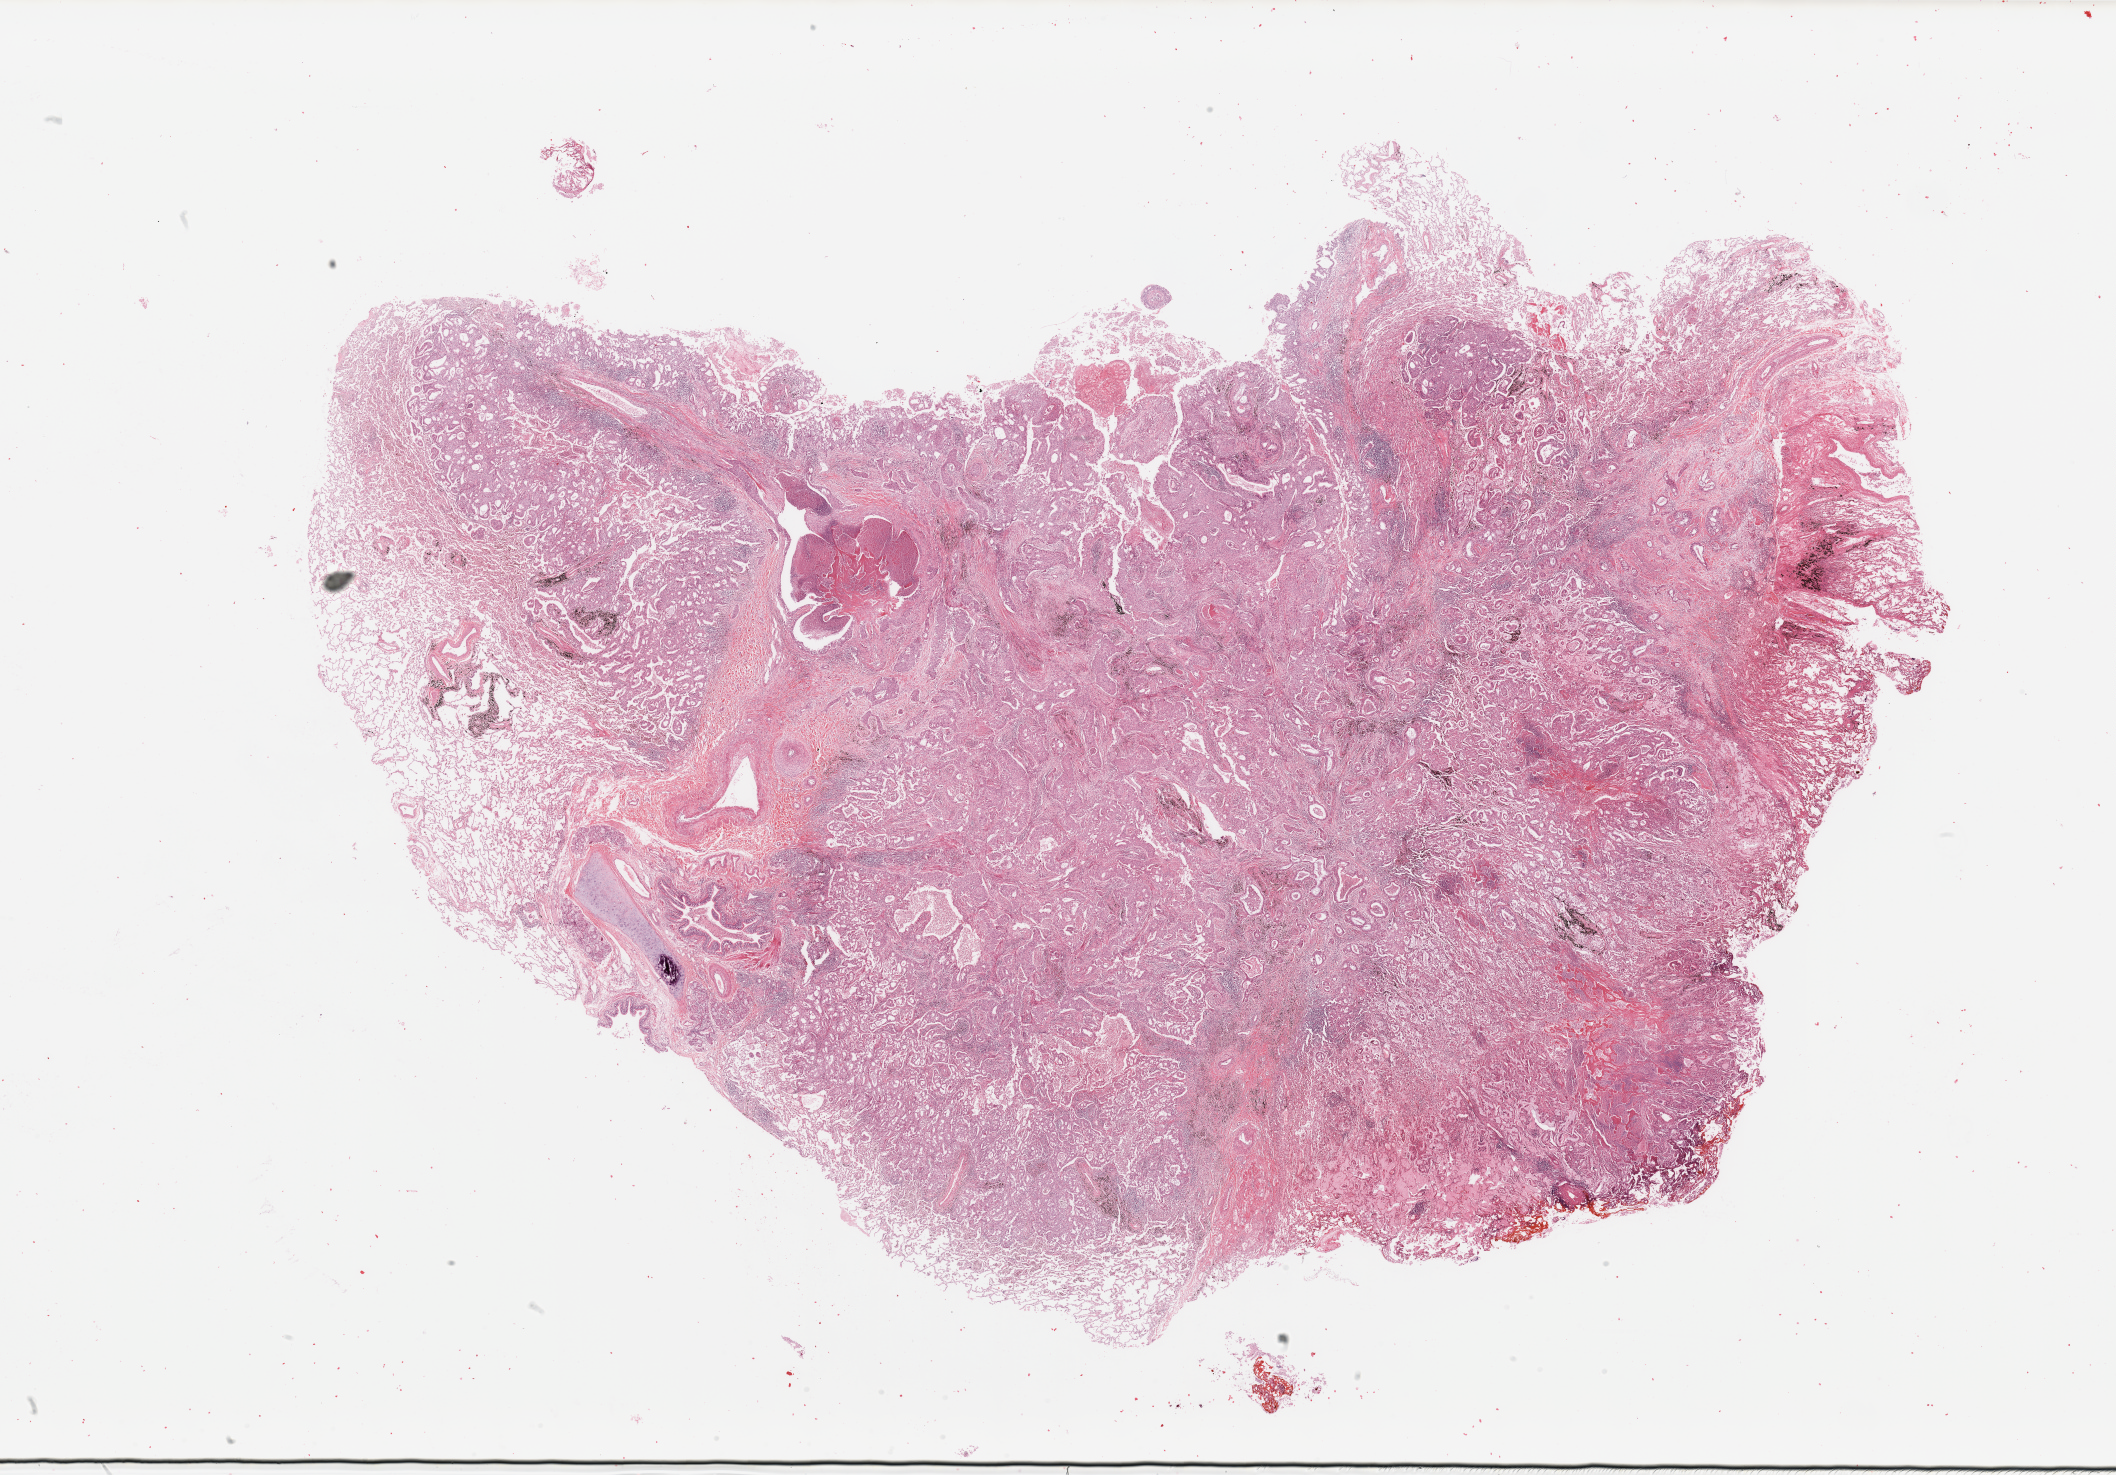
Hematoxylin and eosin (H&E) stained whole-slide image — low-resolution overview of the scanned area, about 33.5 x 23.3 mm (slide scanned at 20x), tumour tissue sample, sampled site: lung. 61-year-old male patient. Histologic grade: G3 (poorly differentiated). Pathologist review of this section (percent, as recorded): tumour nuclei 70%, necrosis 10%.
Diagnosis: Adenocarcinoma, NOS. AJCC pathologic stage: IB.